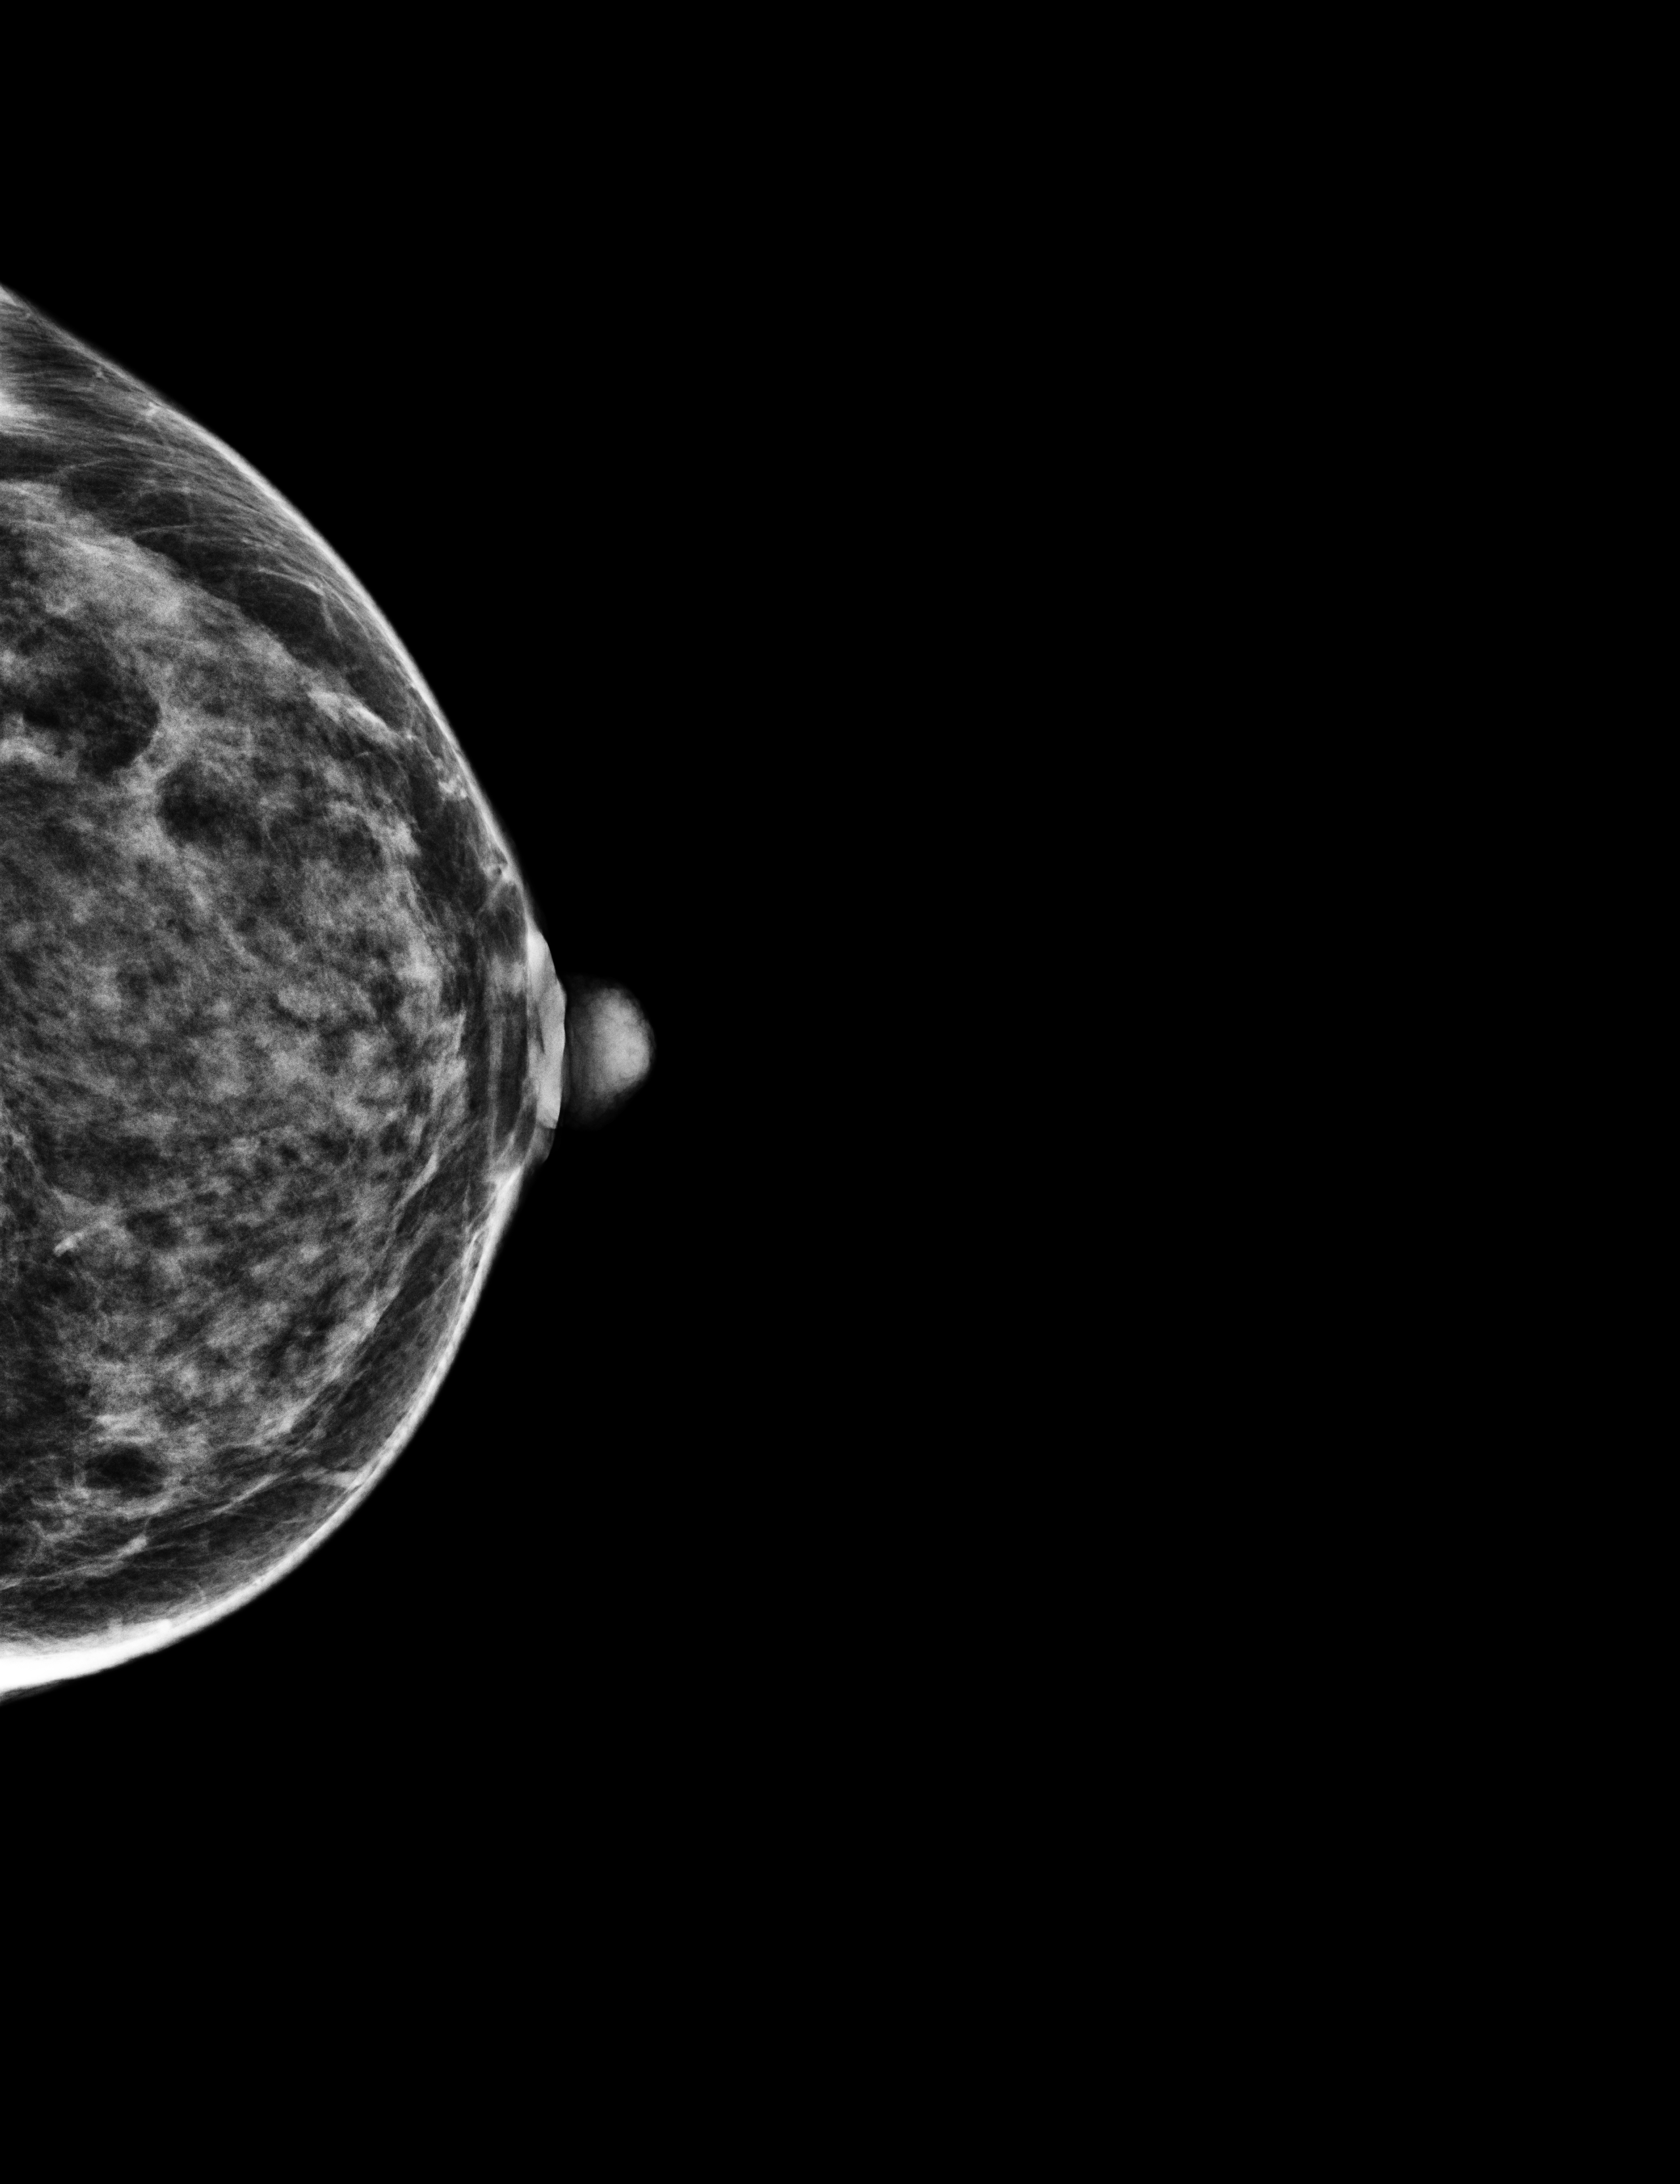
Annual screening mammography examination; compressed breast thickness 37 mm; system: Selenia Dimensions. Female patient, age 43 years.
Image type: full-field digital mammogram. Breast: left. Projection: CC view.